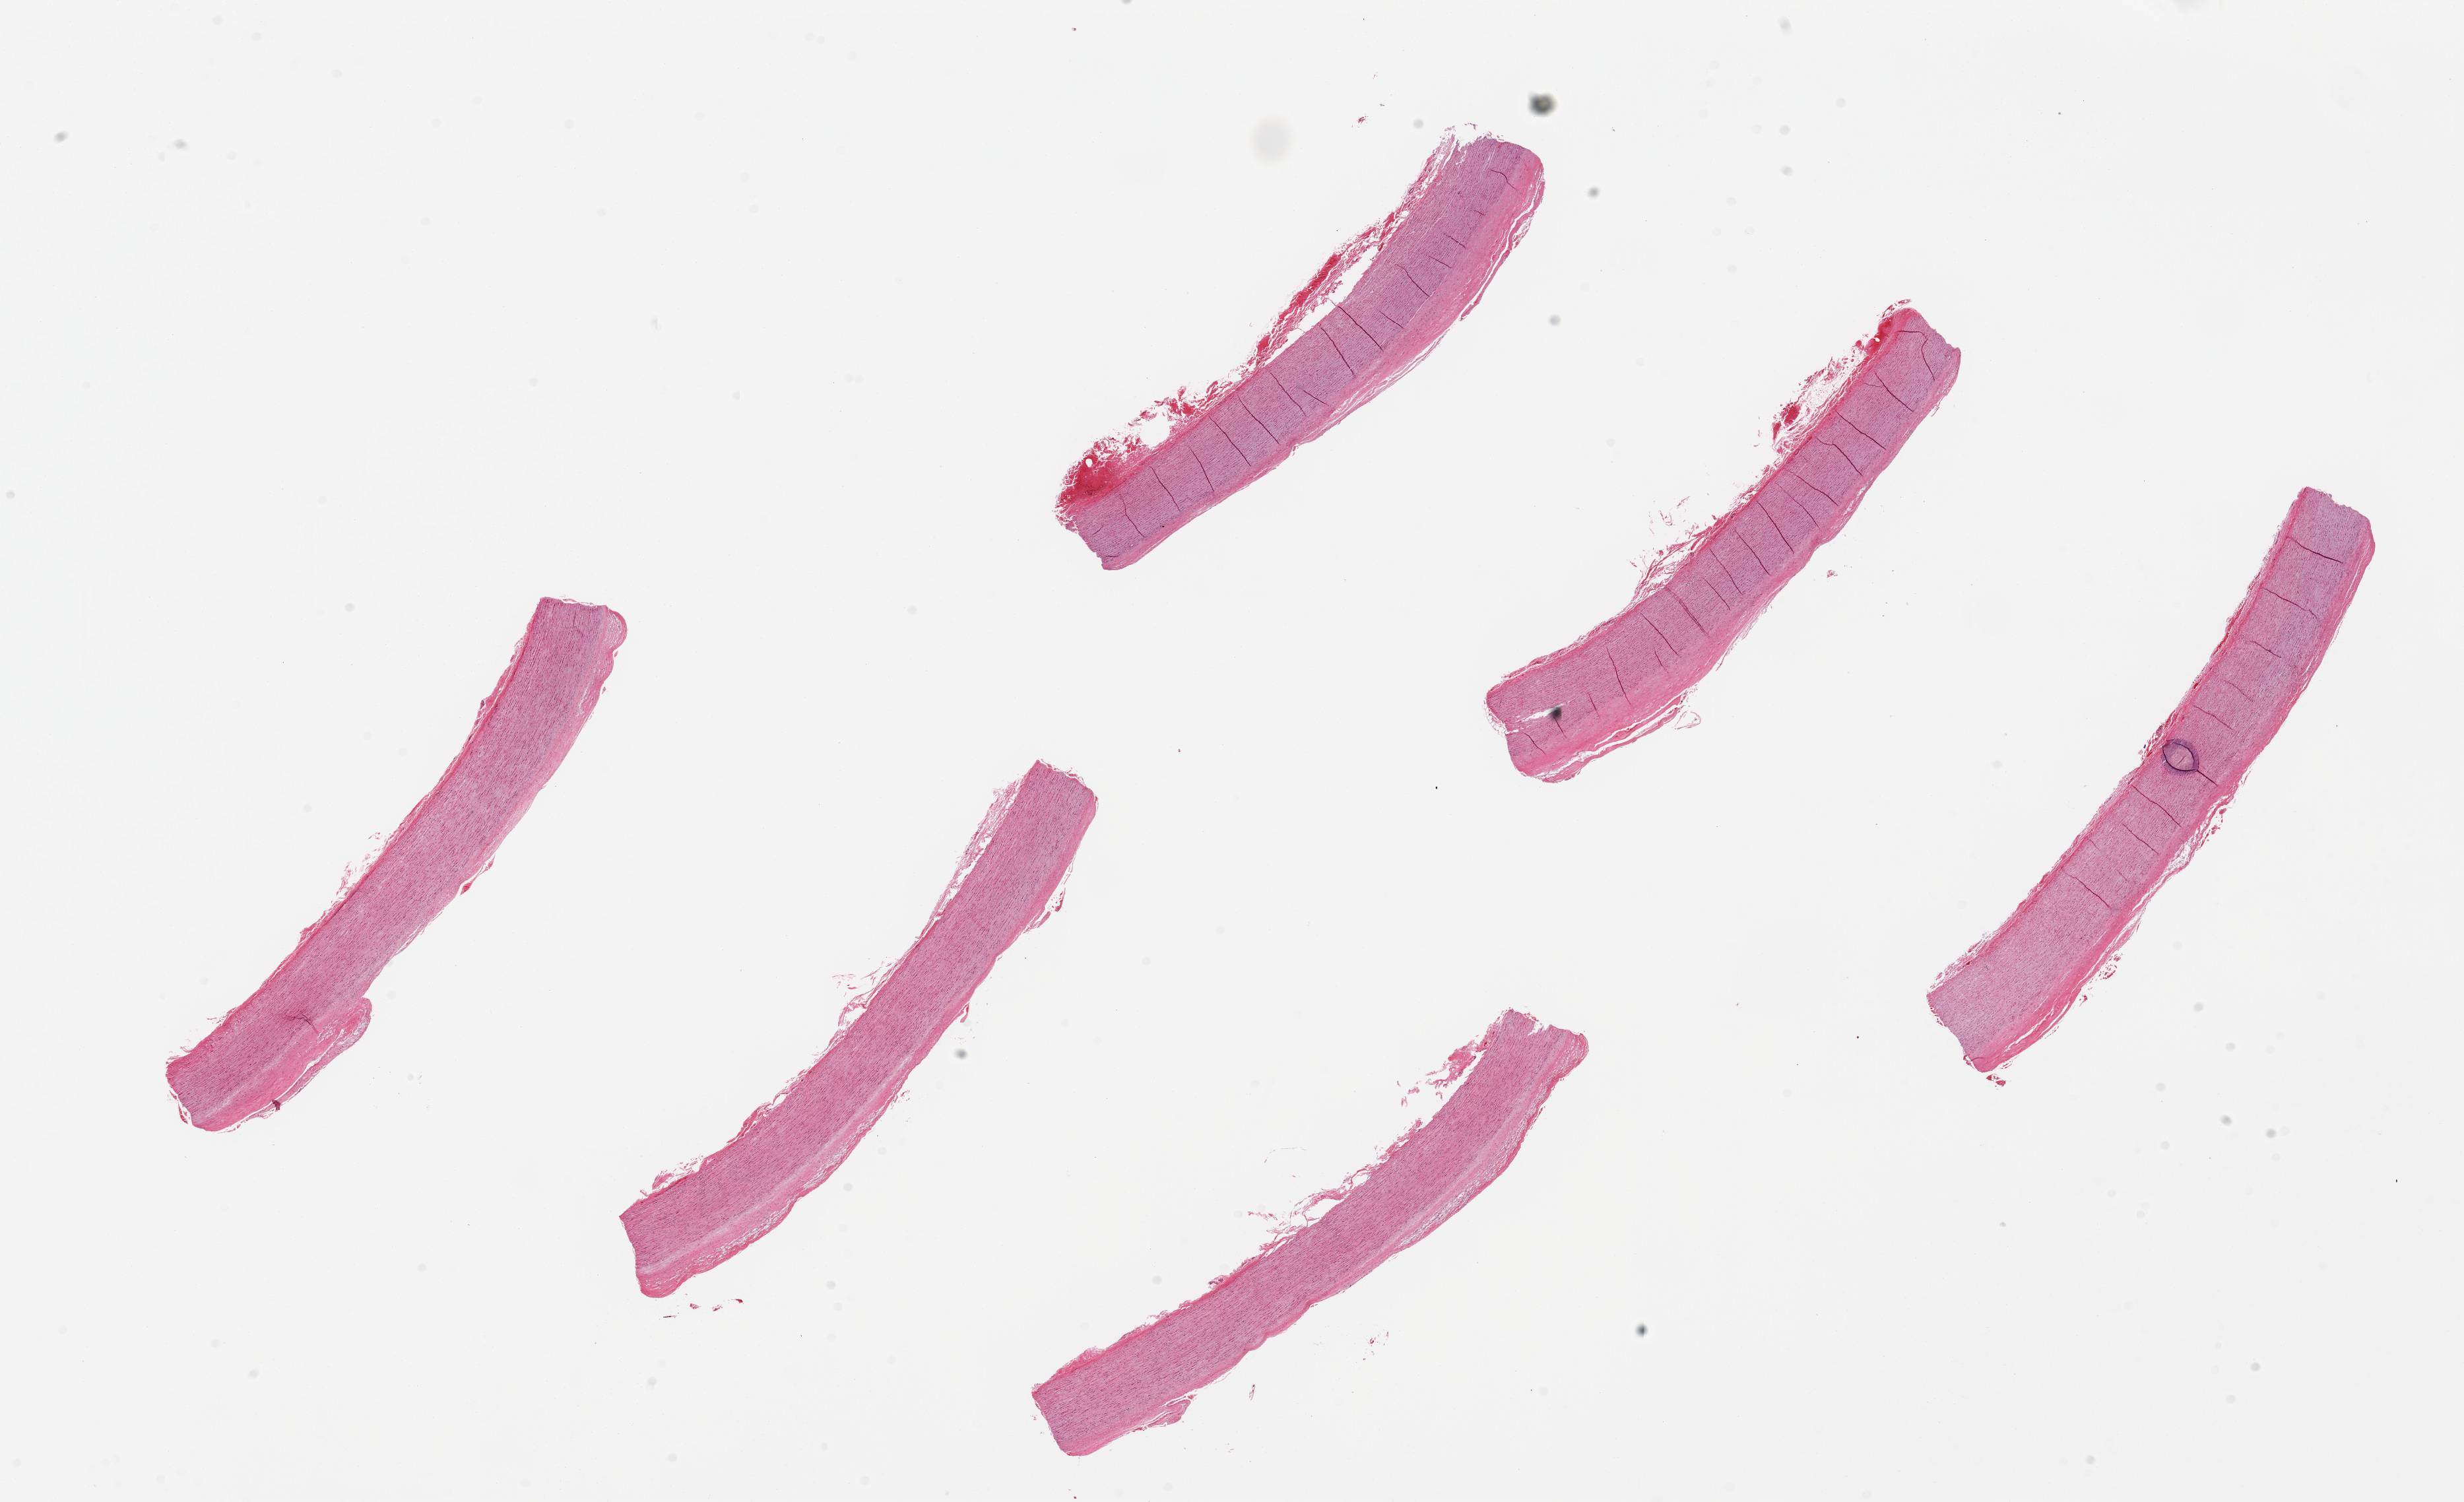
Whole-slide image, H&E stain — a low-resolution overview of the entire scanned area, about 29.5 x 18.0 mm (slide scanned at 20x); PAXgene-fixed, paraffin-embedded tissue; target tissue: aorta; tissue donor sample. Female donor.
Reviewer comment on this tissue sample: 6 pieces. up to 8x1.5mm; well dissected; flat plaques up to 1/3 thickness.